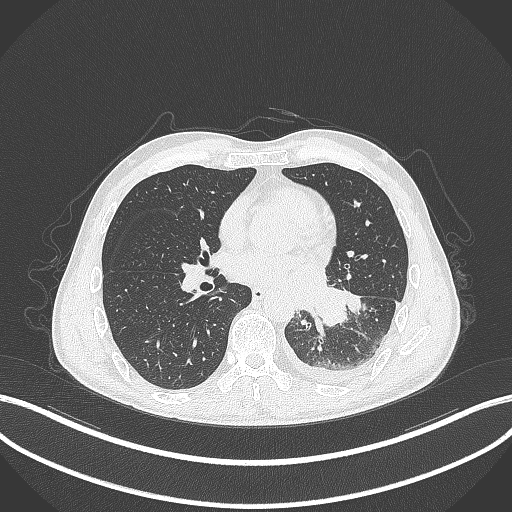
Chest CT, one axial slice. Reconstruction kernel B70f. 120 kVp. Lung window (W 1500 / L -600 HU). 1 mm slice thickness. 512 × 512 image matrix, field of view 400 × 400 mm. Male patient, age 47 years. Case-level facts recorded for this patient, not image findings: clinical TNM (as recorded): T3 N1 M1c.
Outlined on this slice (rectangle marked by the reading radiologist):
- lung tumour (recorded histology: small cell carcinoma): bounding box <310,285,348,330> (left, top, right, bottom; pixels)